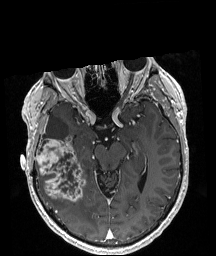
Brain MRI from a brain-tumour surgery series, one axial slice; position 121 of 208 along the scan axis; T1-weighted post-contrast; 1 mm slice thickness; 216 × 256 image matrix. From the clinical record (not read from this slice): histopathology: Astrocytoma; WHO grade: 4; IDH mutation: yes.
Outlined on this slice (expert manual segmentation):
- tumour: bounding box (x1, y1, x2, y2) in pixels: (35, 135, 86, 202)